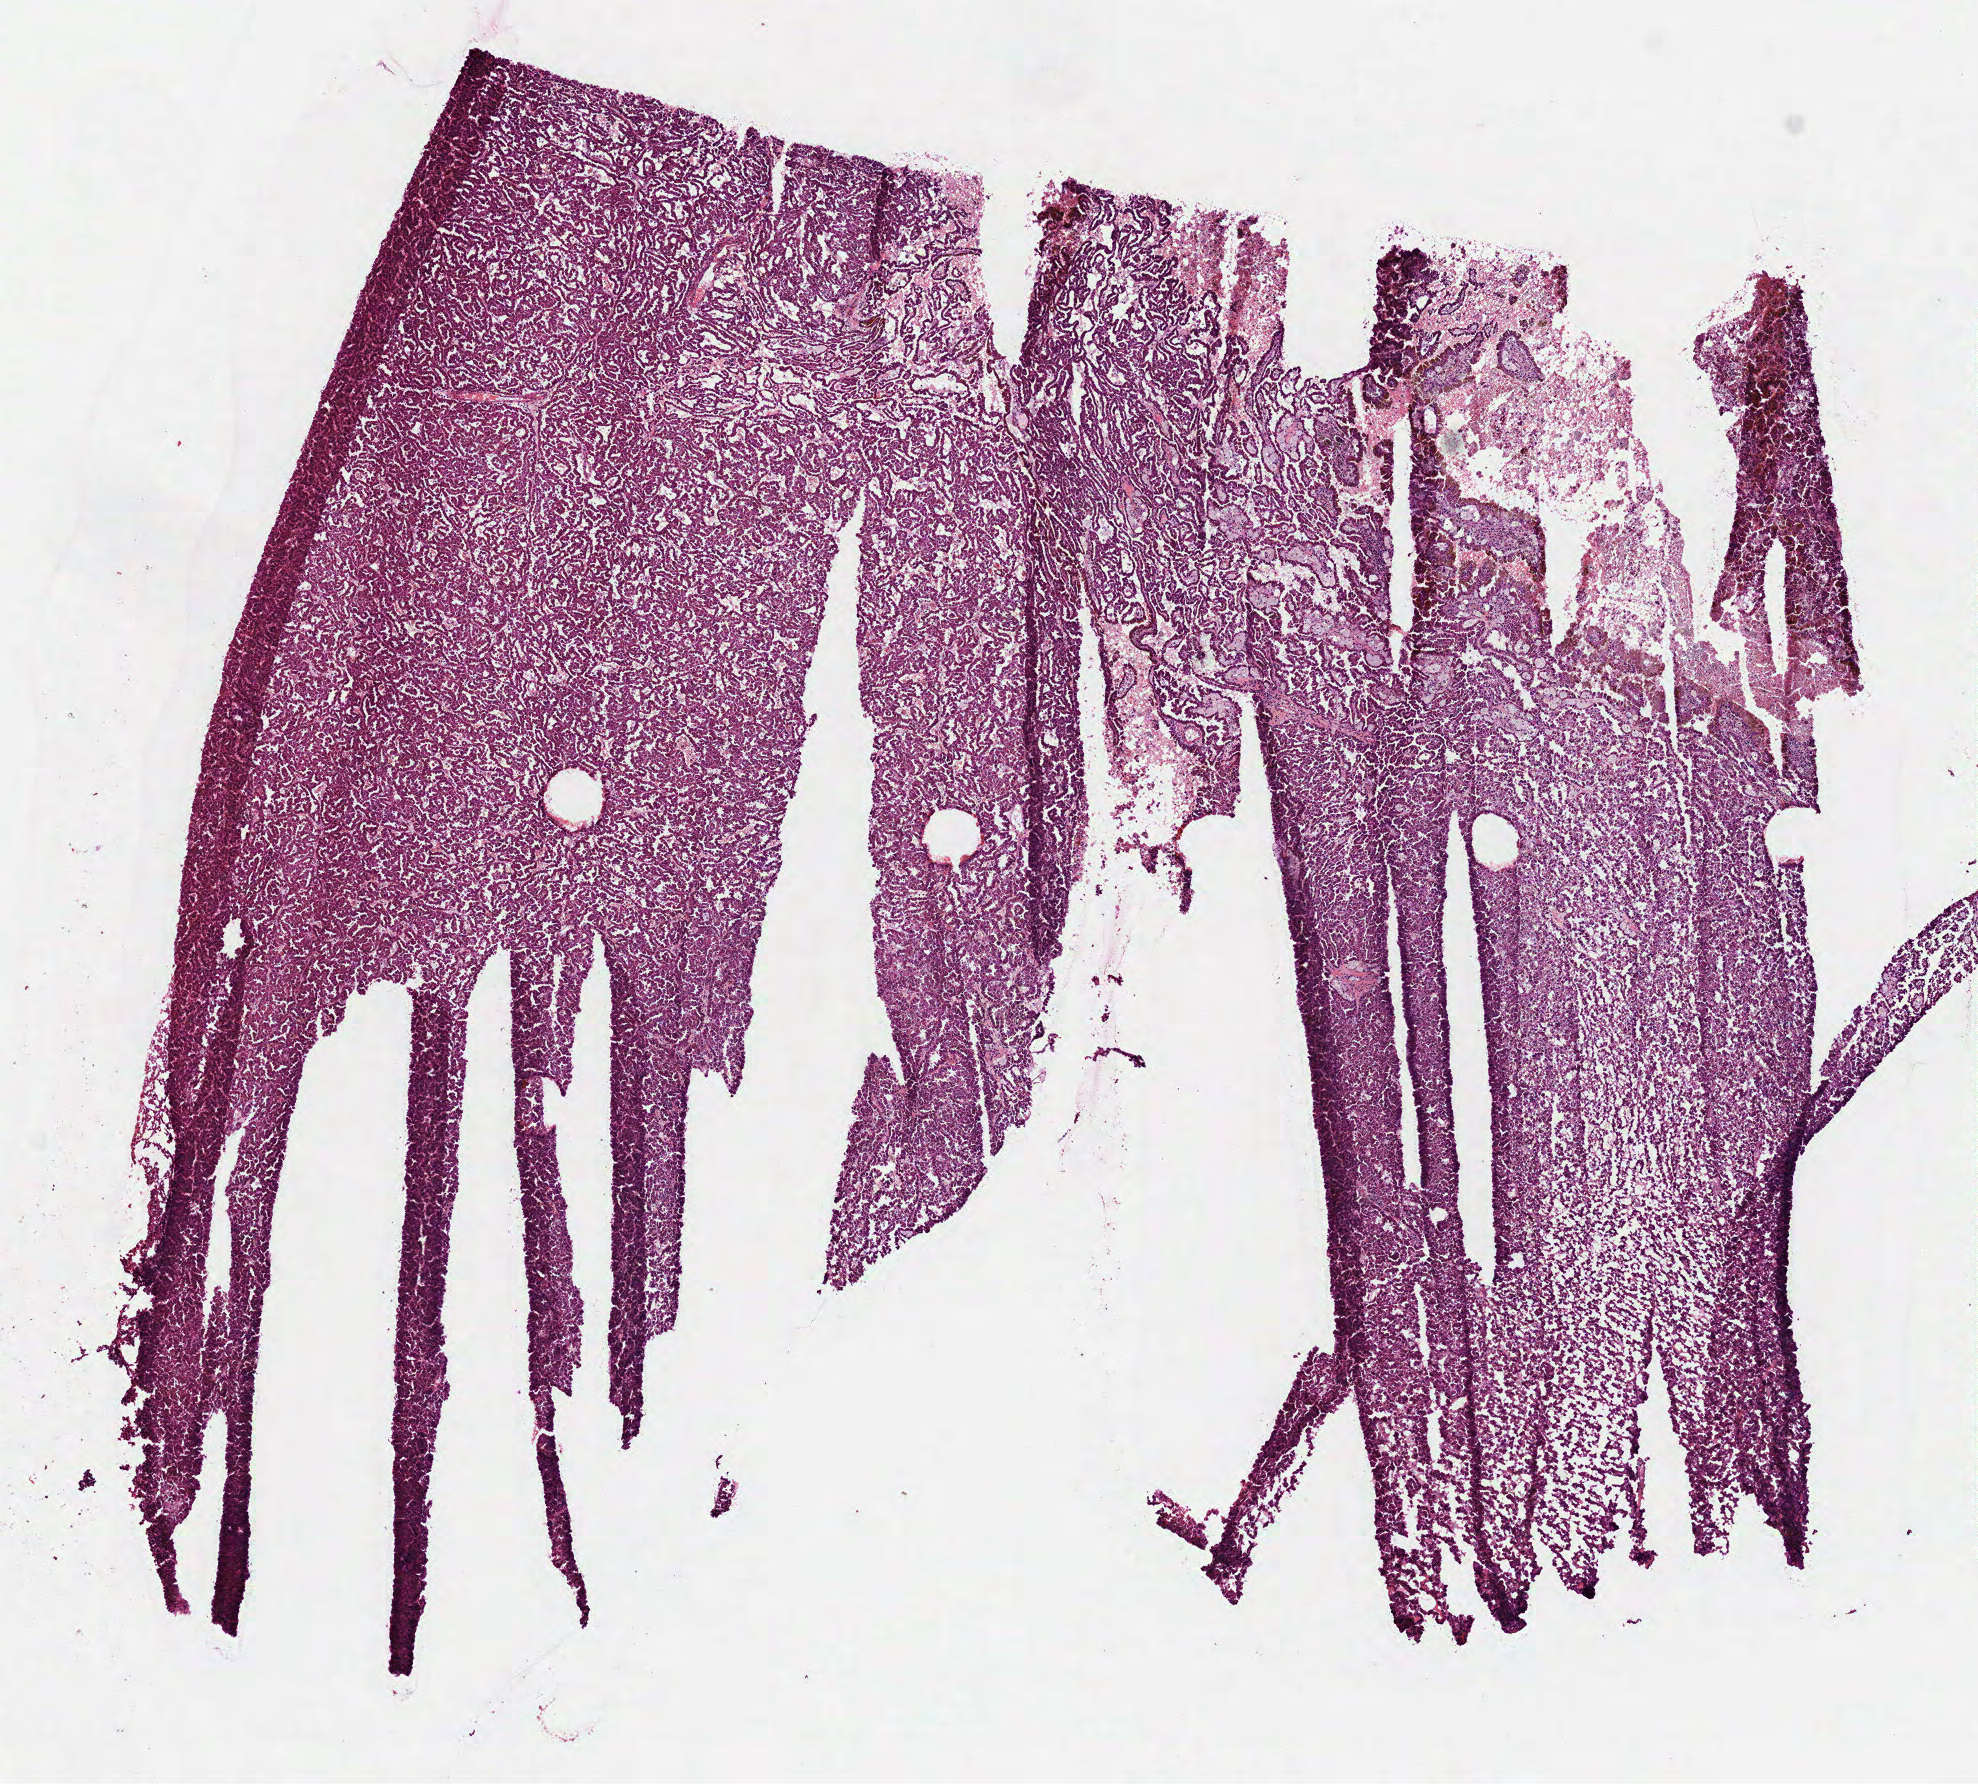
Digitized H&E-stained tissue section (whole slide) — whole scanned area (about 8.0 x 7.2 mm, from a 40x scan) shown as a low-resolution overview. Frozen section from the top of the tissue portion. Kidney, primary tumour sample. Male patient; age at initial diagnosis 59 years. Composition of this section per pathologist review: tumour nuclei 85%, necrosis 10%.
AJCC pathologic stage: I. Diagnosis: Papillary adenocarcinoma, NOS.